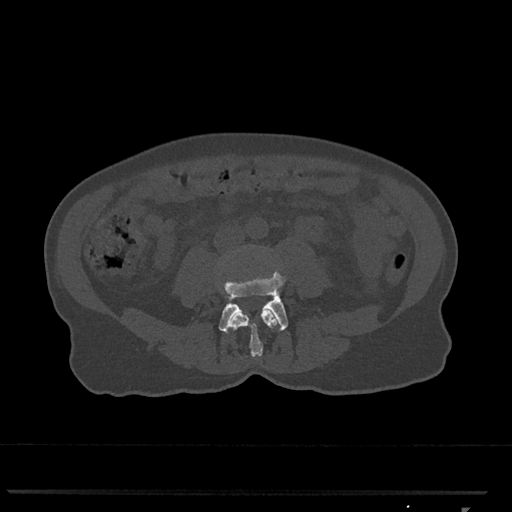
CT including the spine, one axial slice. Slice 235 of 793 in the series (ordered by position). Reconstruction kernel Br40s/3. 120 kVp. Bone window (W 1800 / L 400 HU). 512 × 512 image matrix, field of view 380 × 380 mm. Patient: female, 62 years. Case-level facts recorded for this patient, not image findings: primary cancer: renal.
Outlined on this slice (semi-automatic segmentation, software-assisted and operator-edited):
- L3 vertebra: bounding box <229,309,278,357> (left, top, right, bottom; pixels)
- L4 vertebra: <219,270,288,333>